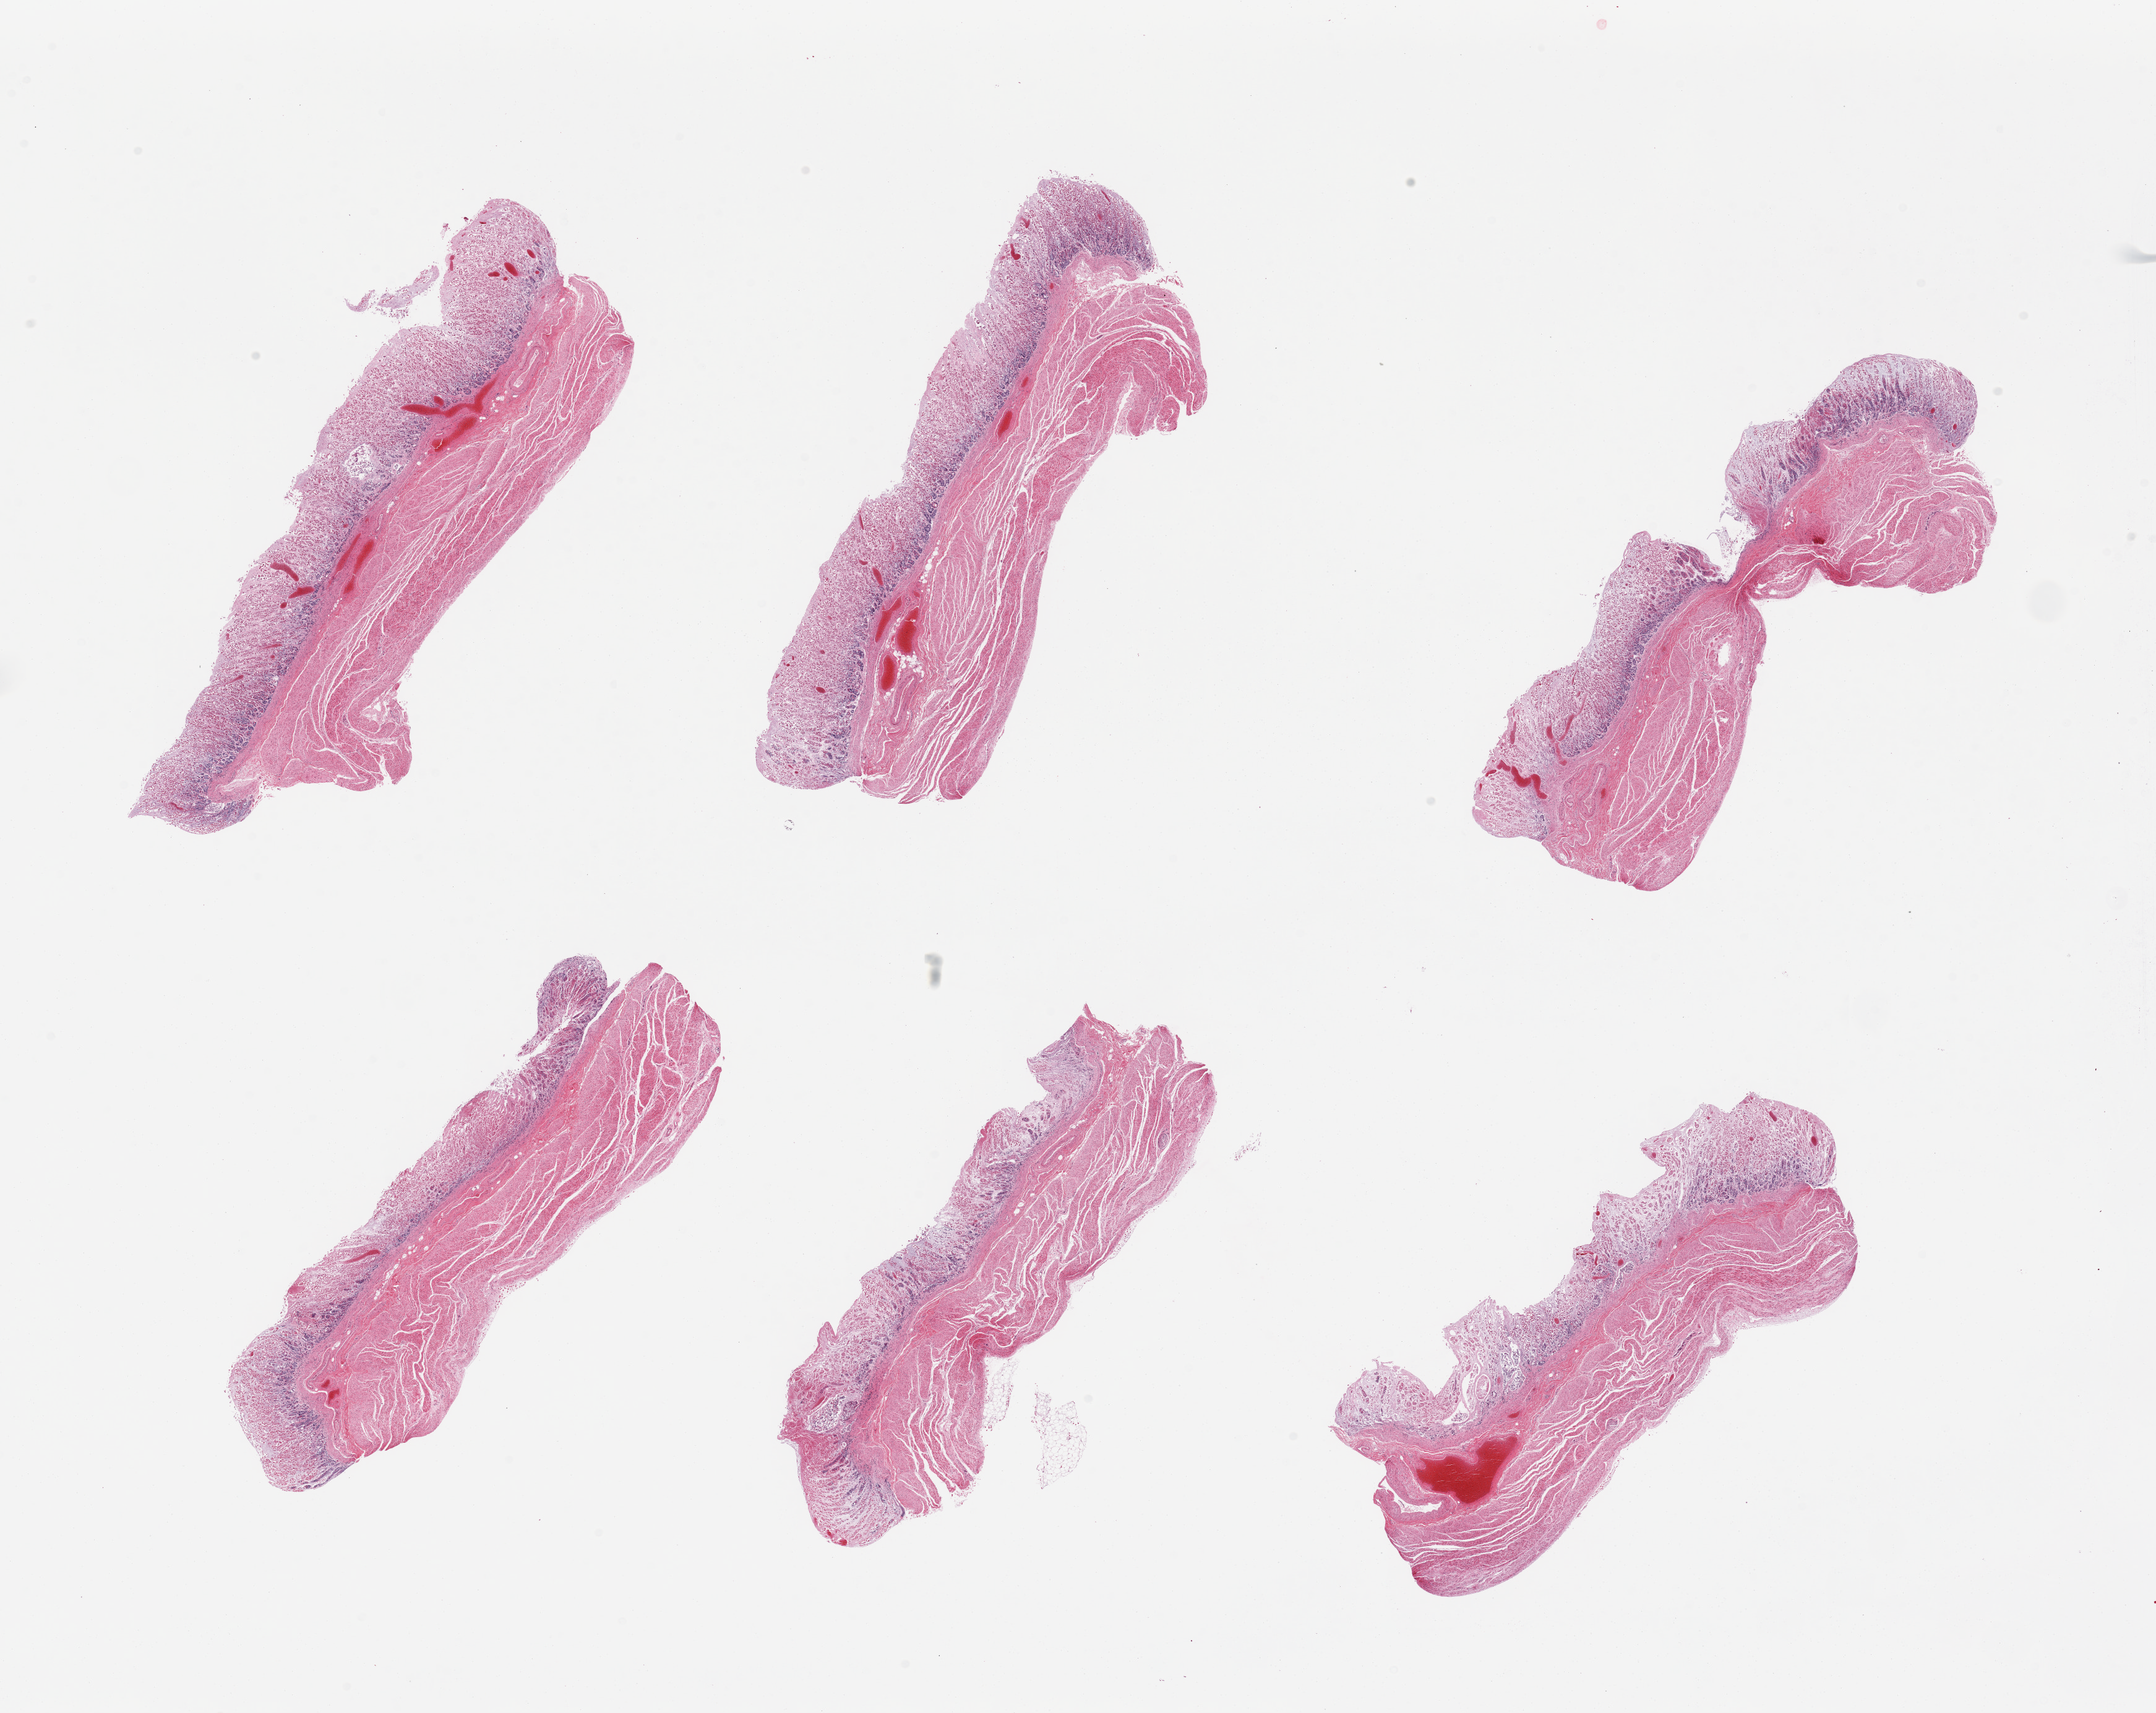
Digitized hematoxylin and eosin (H&E)-stained section — low-resolution overview of the scanned area, about 27.6 x 21.9 mm.
Specimen: PAXgene-fixed paraffin-embedded (PFPE) section; sampled site (target tissue): stomach; donor tissue sample.